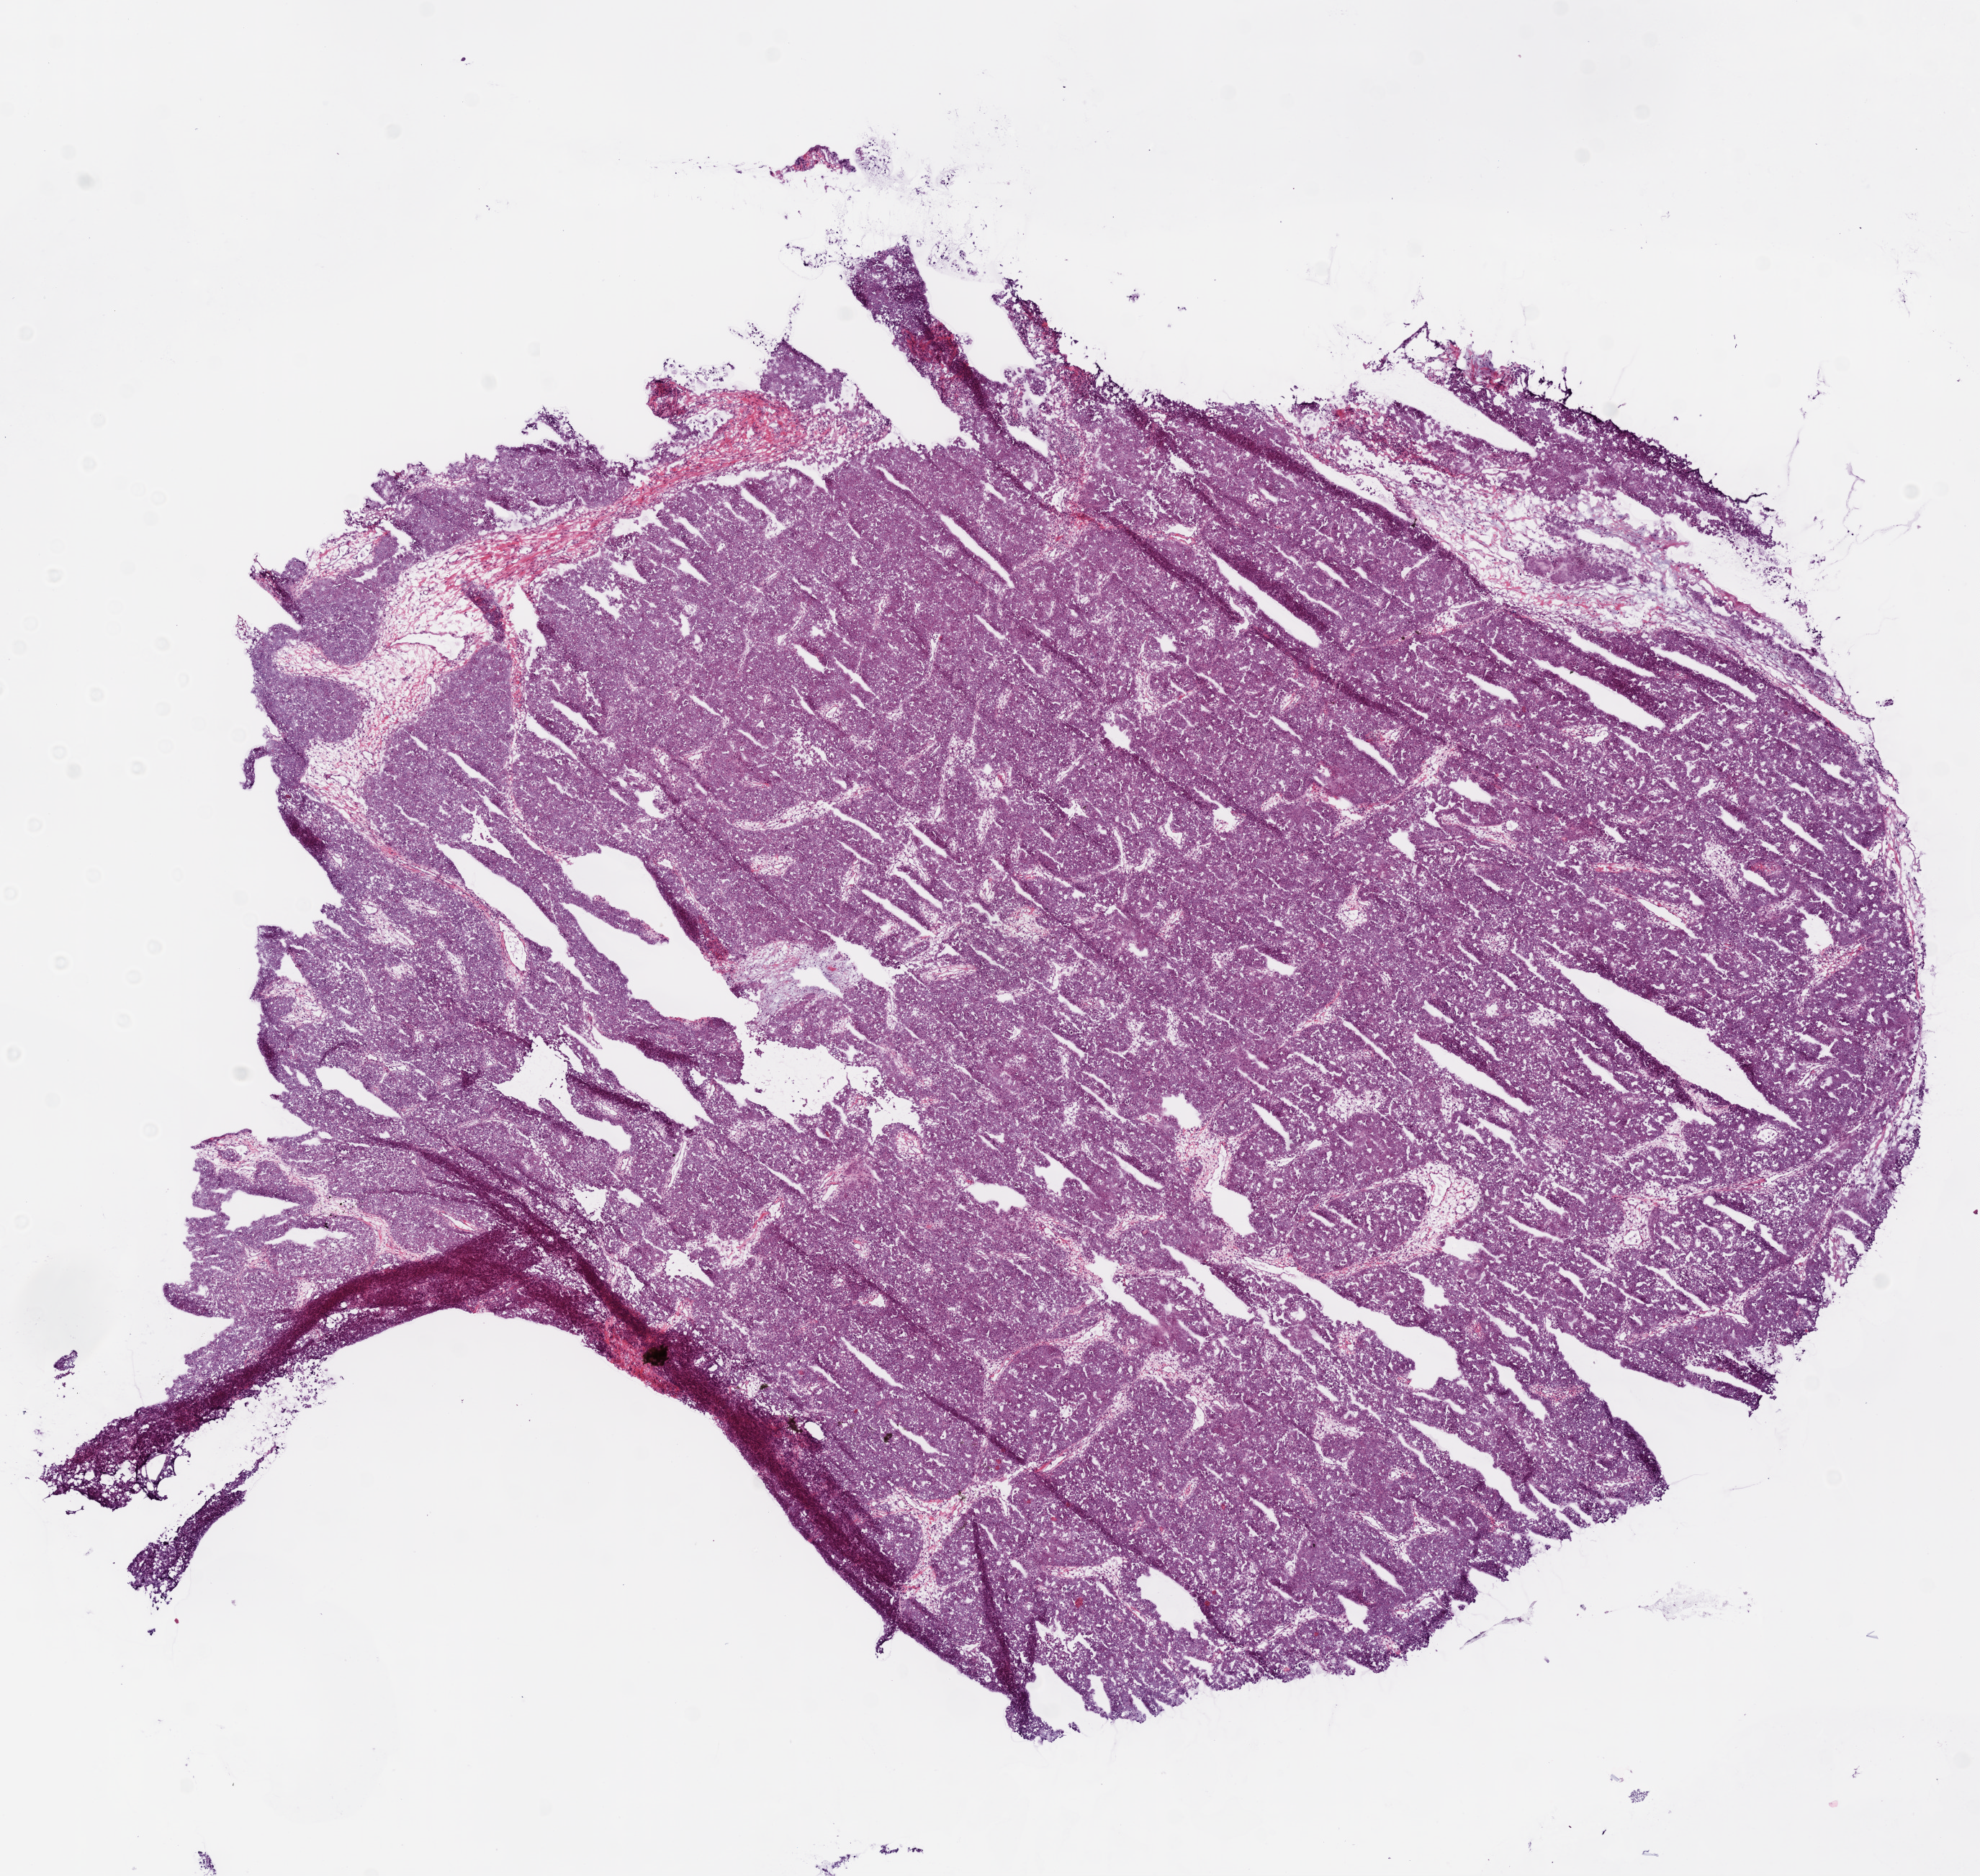
Whole-slide histology image, H&E — whole scanned area (about 11.0 x 10.5 mm, from a 20x scan) shown as a low-resolution overview; frozen section from the bottom of the tissue portion; sample: primary tumour, ovary. Female patient; age at initial diagnosis 60 years. Histologic grade: G3 (poorly differentiated). Slide review estimates, as recorded: tumour cells 90%, tumour nuclei 90%, normal cells 0%, stromal cells 10%, necrosis 0%.
• FIGO stage: IIIC
• histologic diagnosis: Serous cystadenocarcinoma, NOS